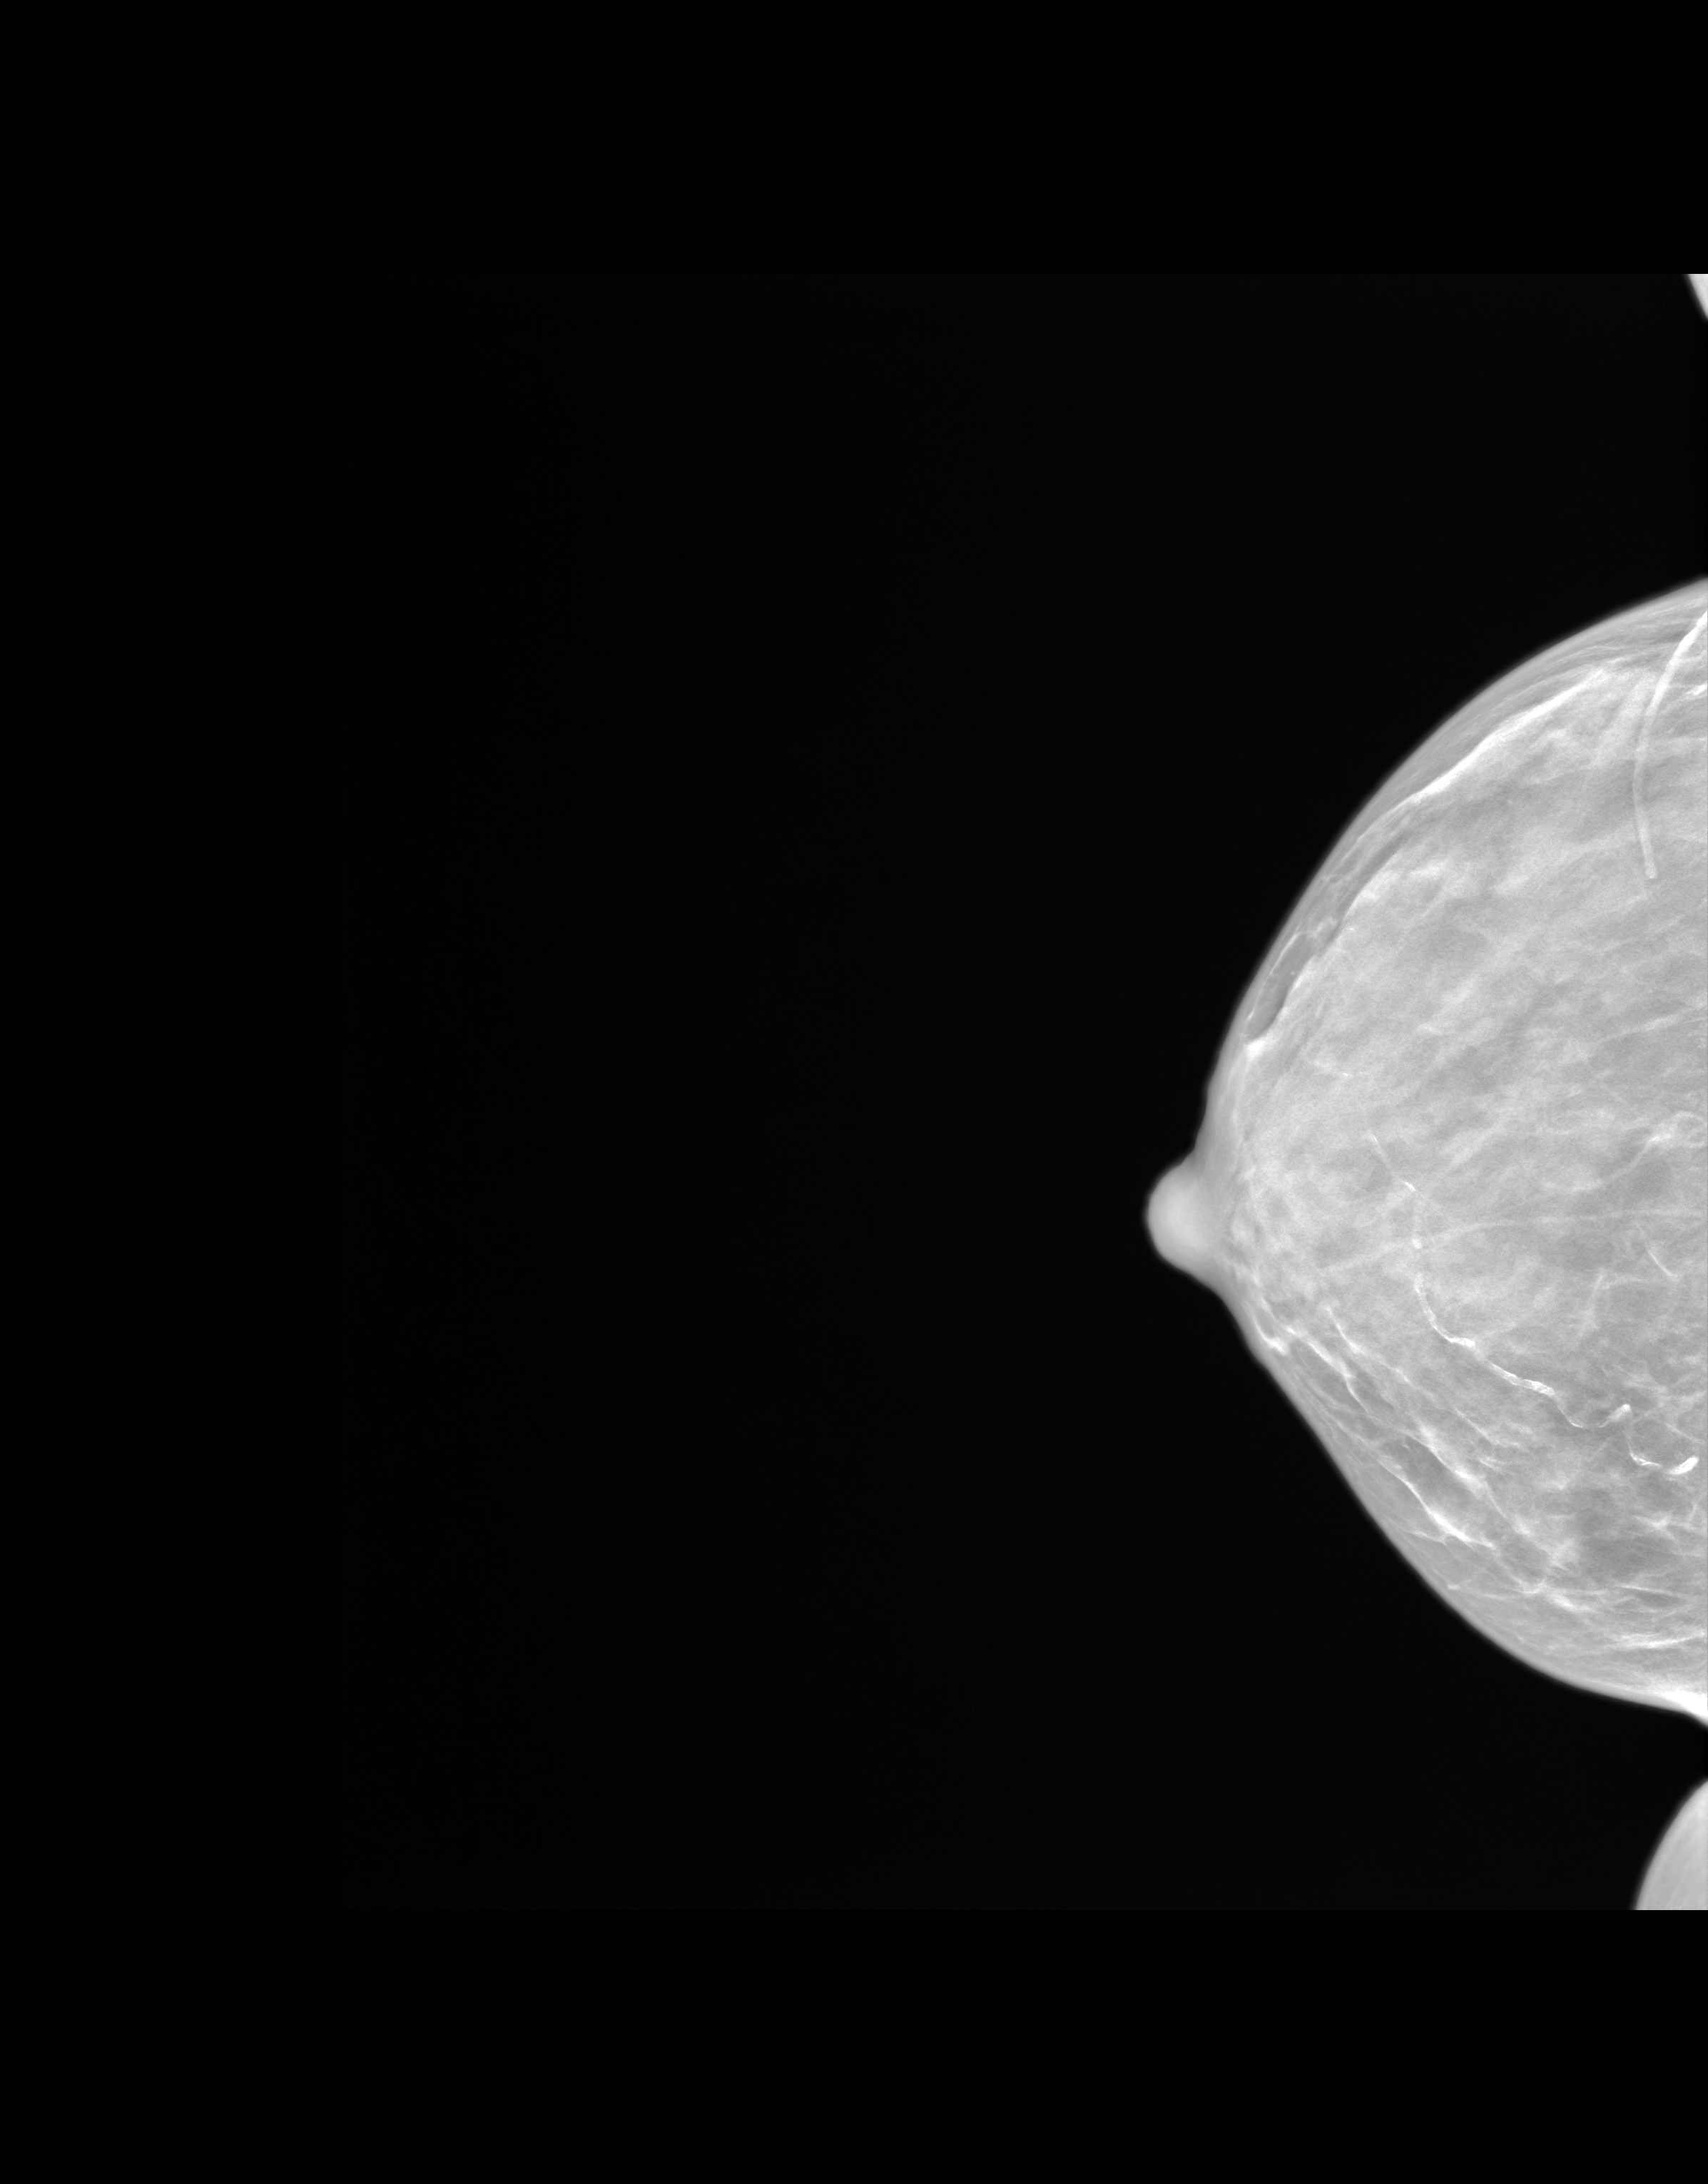
Screening examination. Patient aged 60 years (female).
Image type: synthesized 2-D view from tomosynthesis. Breast: right. Projection: CC view.